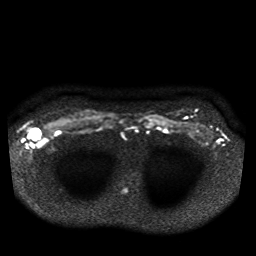
Breast MRI, one axial slice. Slice 34 of 41 in the series (ordered by position). Diffusion-weighted series; image 2 of 4 stored at this slice position (different b-values; order by instance number). 1.5 T. 5 mm slice thickness. 256 × 256 image matrix, field of view 330 × 330 mm. Female patient.
Annotated regions visible in this slice (manually delineated by an expert):
- tumour on diffusion-weighted imaging: bounding box (x1, y1, x2, y2) in pixels: (29, 129, 40, 140)